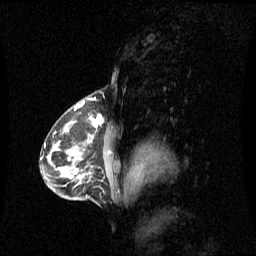
Breast MRI (dynamic contrast-enhanced), one sagittal slice. Position 42 of 60 along the scan axis. Dynamic contrast-enhanced series, image 2 of 3 at this slice position (ordered by acquisition). 1.5 T. TE 4.2 ms, TR 8.4 ms. 2 mm slice thickness. 256 × 256 image matrix. Patient: female, 42 years. From the clinical record (not read from this slice): setting: breast cancer imaged before/during neoadjuvant chemotherapy; receptor status: HR-positive, HER2-negative.
Outlined on this slice (semi-automatic segmentation, software-assisted and operator-edited):
- analysis volume of interest (the breast-tissue region the enhancement analysis was run in; not a lesion): bounding box (x1, y1, x2, y2) in pixels: (56, 113, 120, 185)
- tumour enhancement mask (voxels above the 70 % enhancement threshold inside the analysis volume of interest): (67, 115, 103, 178)